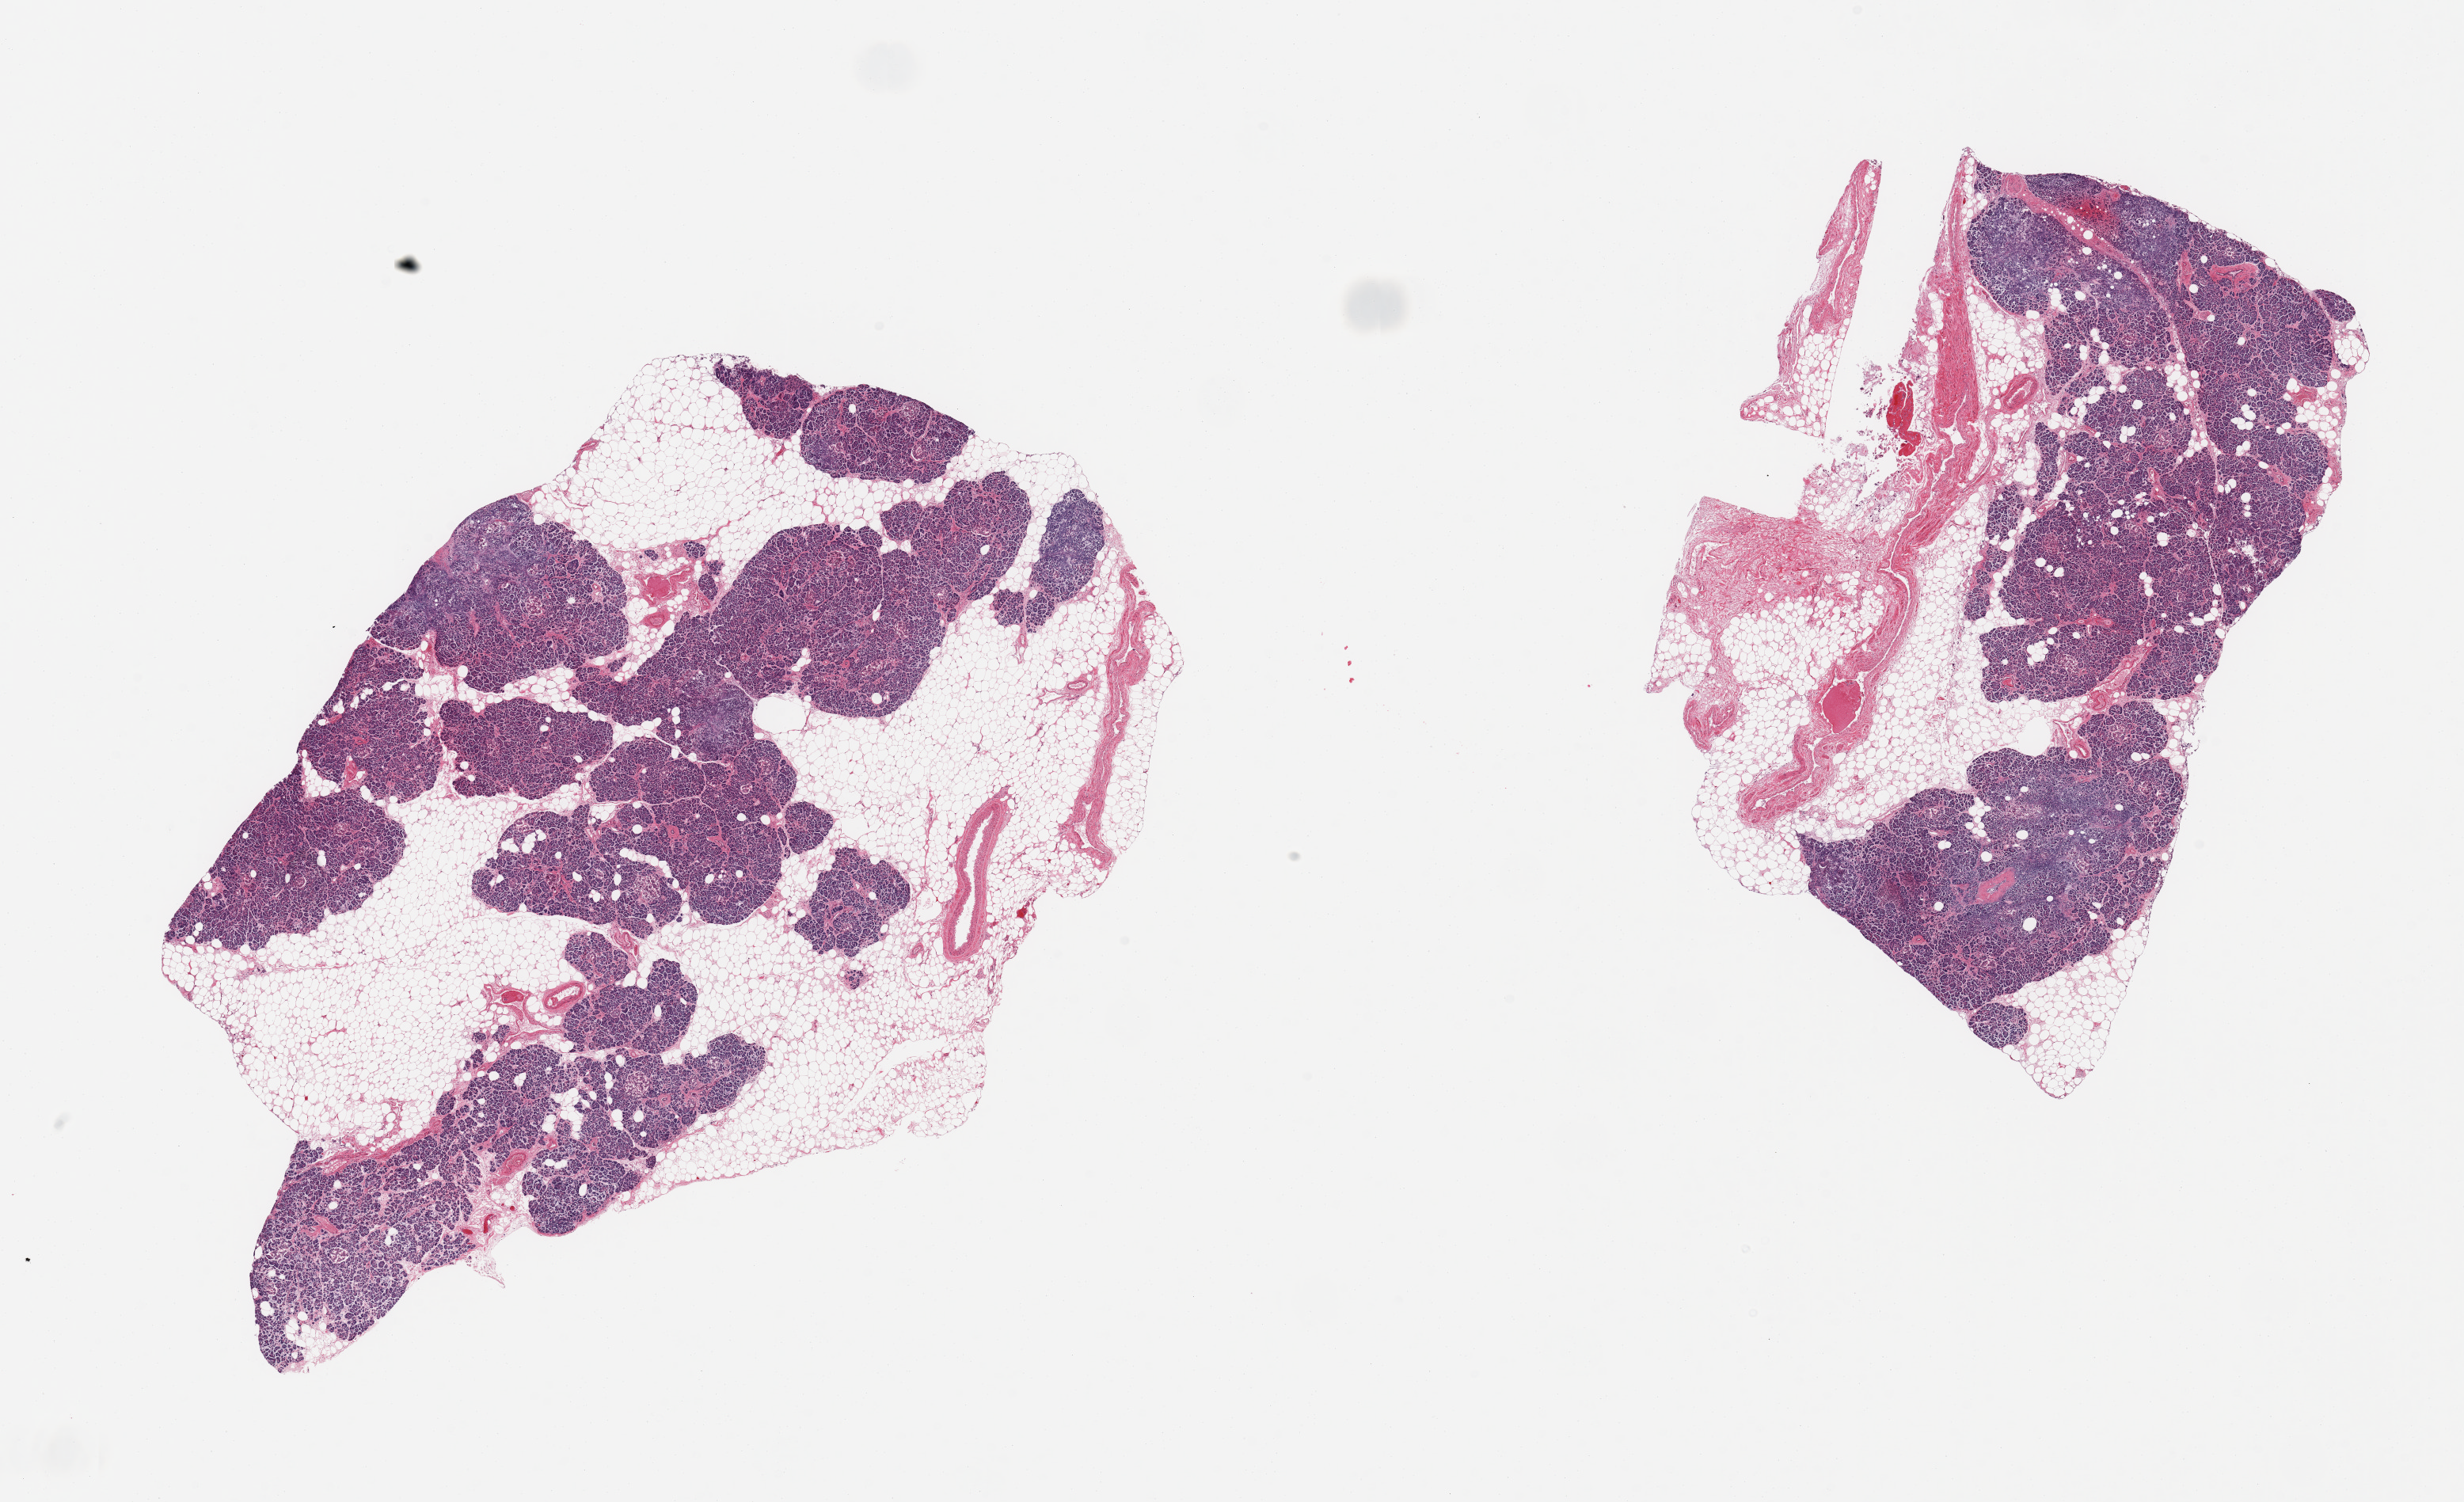
Whole-slide image, H&E stain, whole scanned area (about 24.6 x 15.0 mm) shown as a low-resolution overview; PAXgene-fixed paraffin-embedded (PFPE) section; section of pancreas (target tissue); donor tissue sample. Donor sex: male.
Pathologist's review note for this sample: 2 pieces; some areas have slight autolysis; 50% internal & external fatty and fibrofatty content.